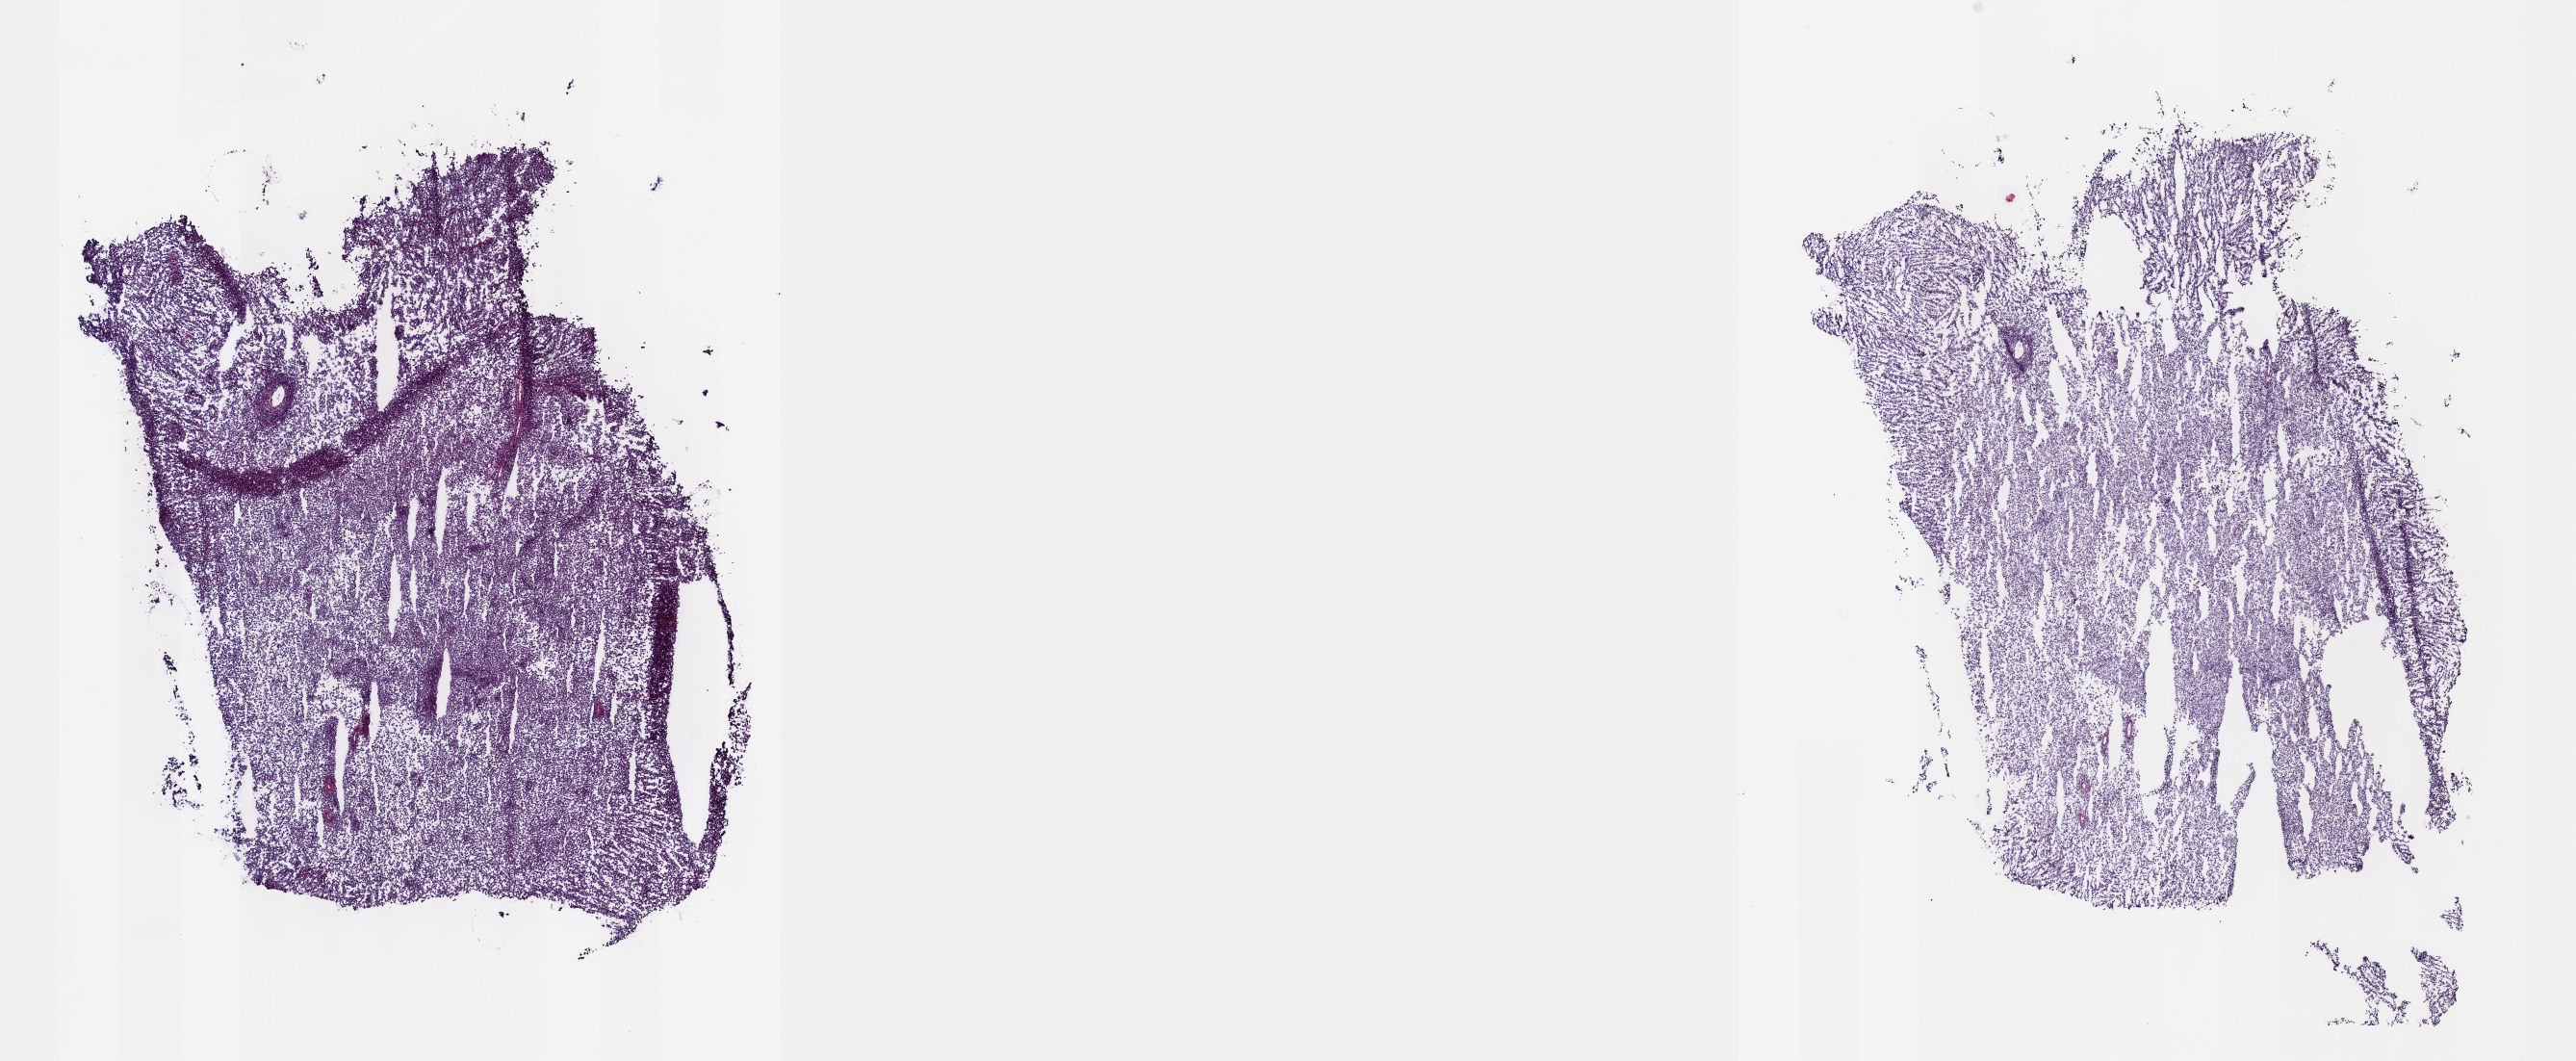
Digitized H&E-stained tissue section (whole slide), shown as a low-resolution overview of the whole scanned area (about 21.6 x 8.9 mm, slide scanned at 40x). Frozen section from the top of the tissue portion. Primary tumour sample from the testis. Male, age 37 years at initial diagnosis. Pathologist review of this section (percent, as recorded): tumour cells 89%, tumour nuclei 94%, normal cells 0%, stromal cells 3%, necrosis 8%. Infiltration values recorded for this section: lymphocyte infiltration 5%, monocyte infiltration 0%, neutrophil infiltration 0%.
Pathologic diagnosis: Seminoma, NOS. AJCC pathologic stage: IS (7th edition).